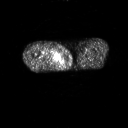
FDG PET of an extremity soft-tissue mass (from a PET/CT study), one axial slice; position 241 of 311 along the scan axis; 3.27 mm slice thickness; 128 × 128 image matrix, field of view 700 × 700 mm. Patient: male, 50 years. From the clinical record (not read from this slice): histological type: undifferentiated - pleiomorphic; grade: high; site of the primary tumour: right thigh.
Outlined on this slice (expert contour drawn on MRI and transferred to this co-registered scan by the dataset authors):
- gross tumour volume including surrounding oedema: bounding box <41,49,57,61> (left, top, right, bottom; pixels)
- gross tumour volume (mass): <49,52,57,59>